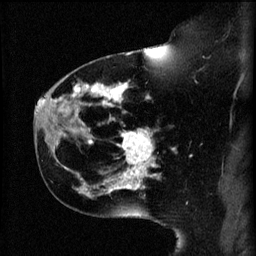
Breast MRI (dynamic contrast-enhanced), one sagittal slice. Slice 39 of 60 in the series (ordered by position). 3 images stored at this slice position (order not interpretable as contrast timing). 1.5 T. TE 4.2 ms, TR 11 ms. 256 × 256 image matrix, field of view 180 × 180 mm. Female patient, age 44 years.
Outlined on this slice (semi-automatic segmentation, software-assisted and operator-edited):
- analysis volume of interest (the breast-tissue region the enhancement analysis was run in; not a lesion): bounding box <110,130,159,179> (left, top, right, bottom; pixels)
- tumour enhancement mask (voxels above the 70 % enhancement threshold inside the analysis volume of interest): <120,130,157,179>